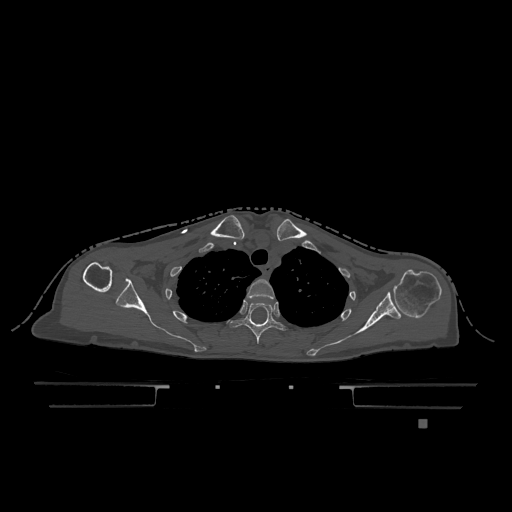
CT including the spine, one axial slice; slice 932 of 1317 in the series (ordered by position); bone window (W 1800 / L 400 HU); 0.5 mm slice thickness; 512 × 512 image matrix. Patient: female, 74 years. Case-level facts recorded for this patient, not image findings: primary cancer: lung; vertebrae with lytic lesions (as recorded): T1, T4, T5, T6, L4, L5.
Outlined on this slice (semi-automatic segmentation, software-assisted and operator-edited):
- T2 vertebra: bounding box (x1, y1, x2, y2) in pixels: (247, 279, 275, 299)
- T3 vertebra: (230, 302, 287, 344)